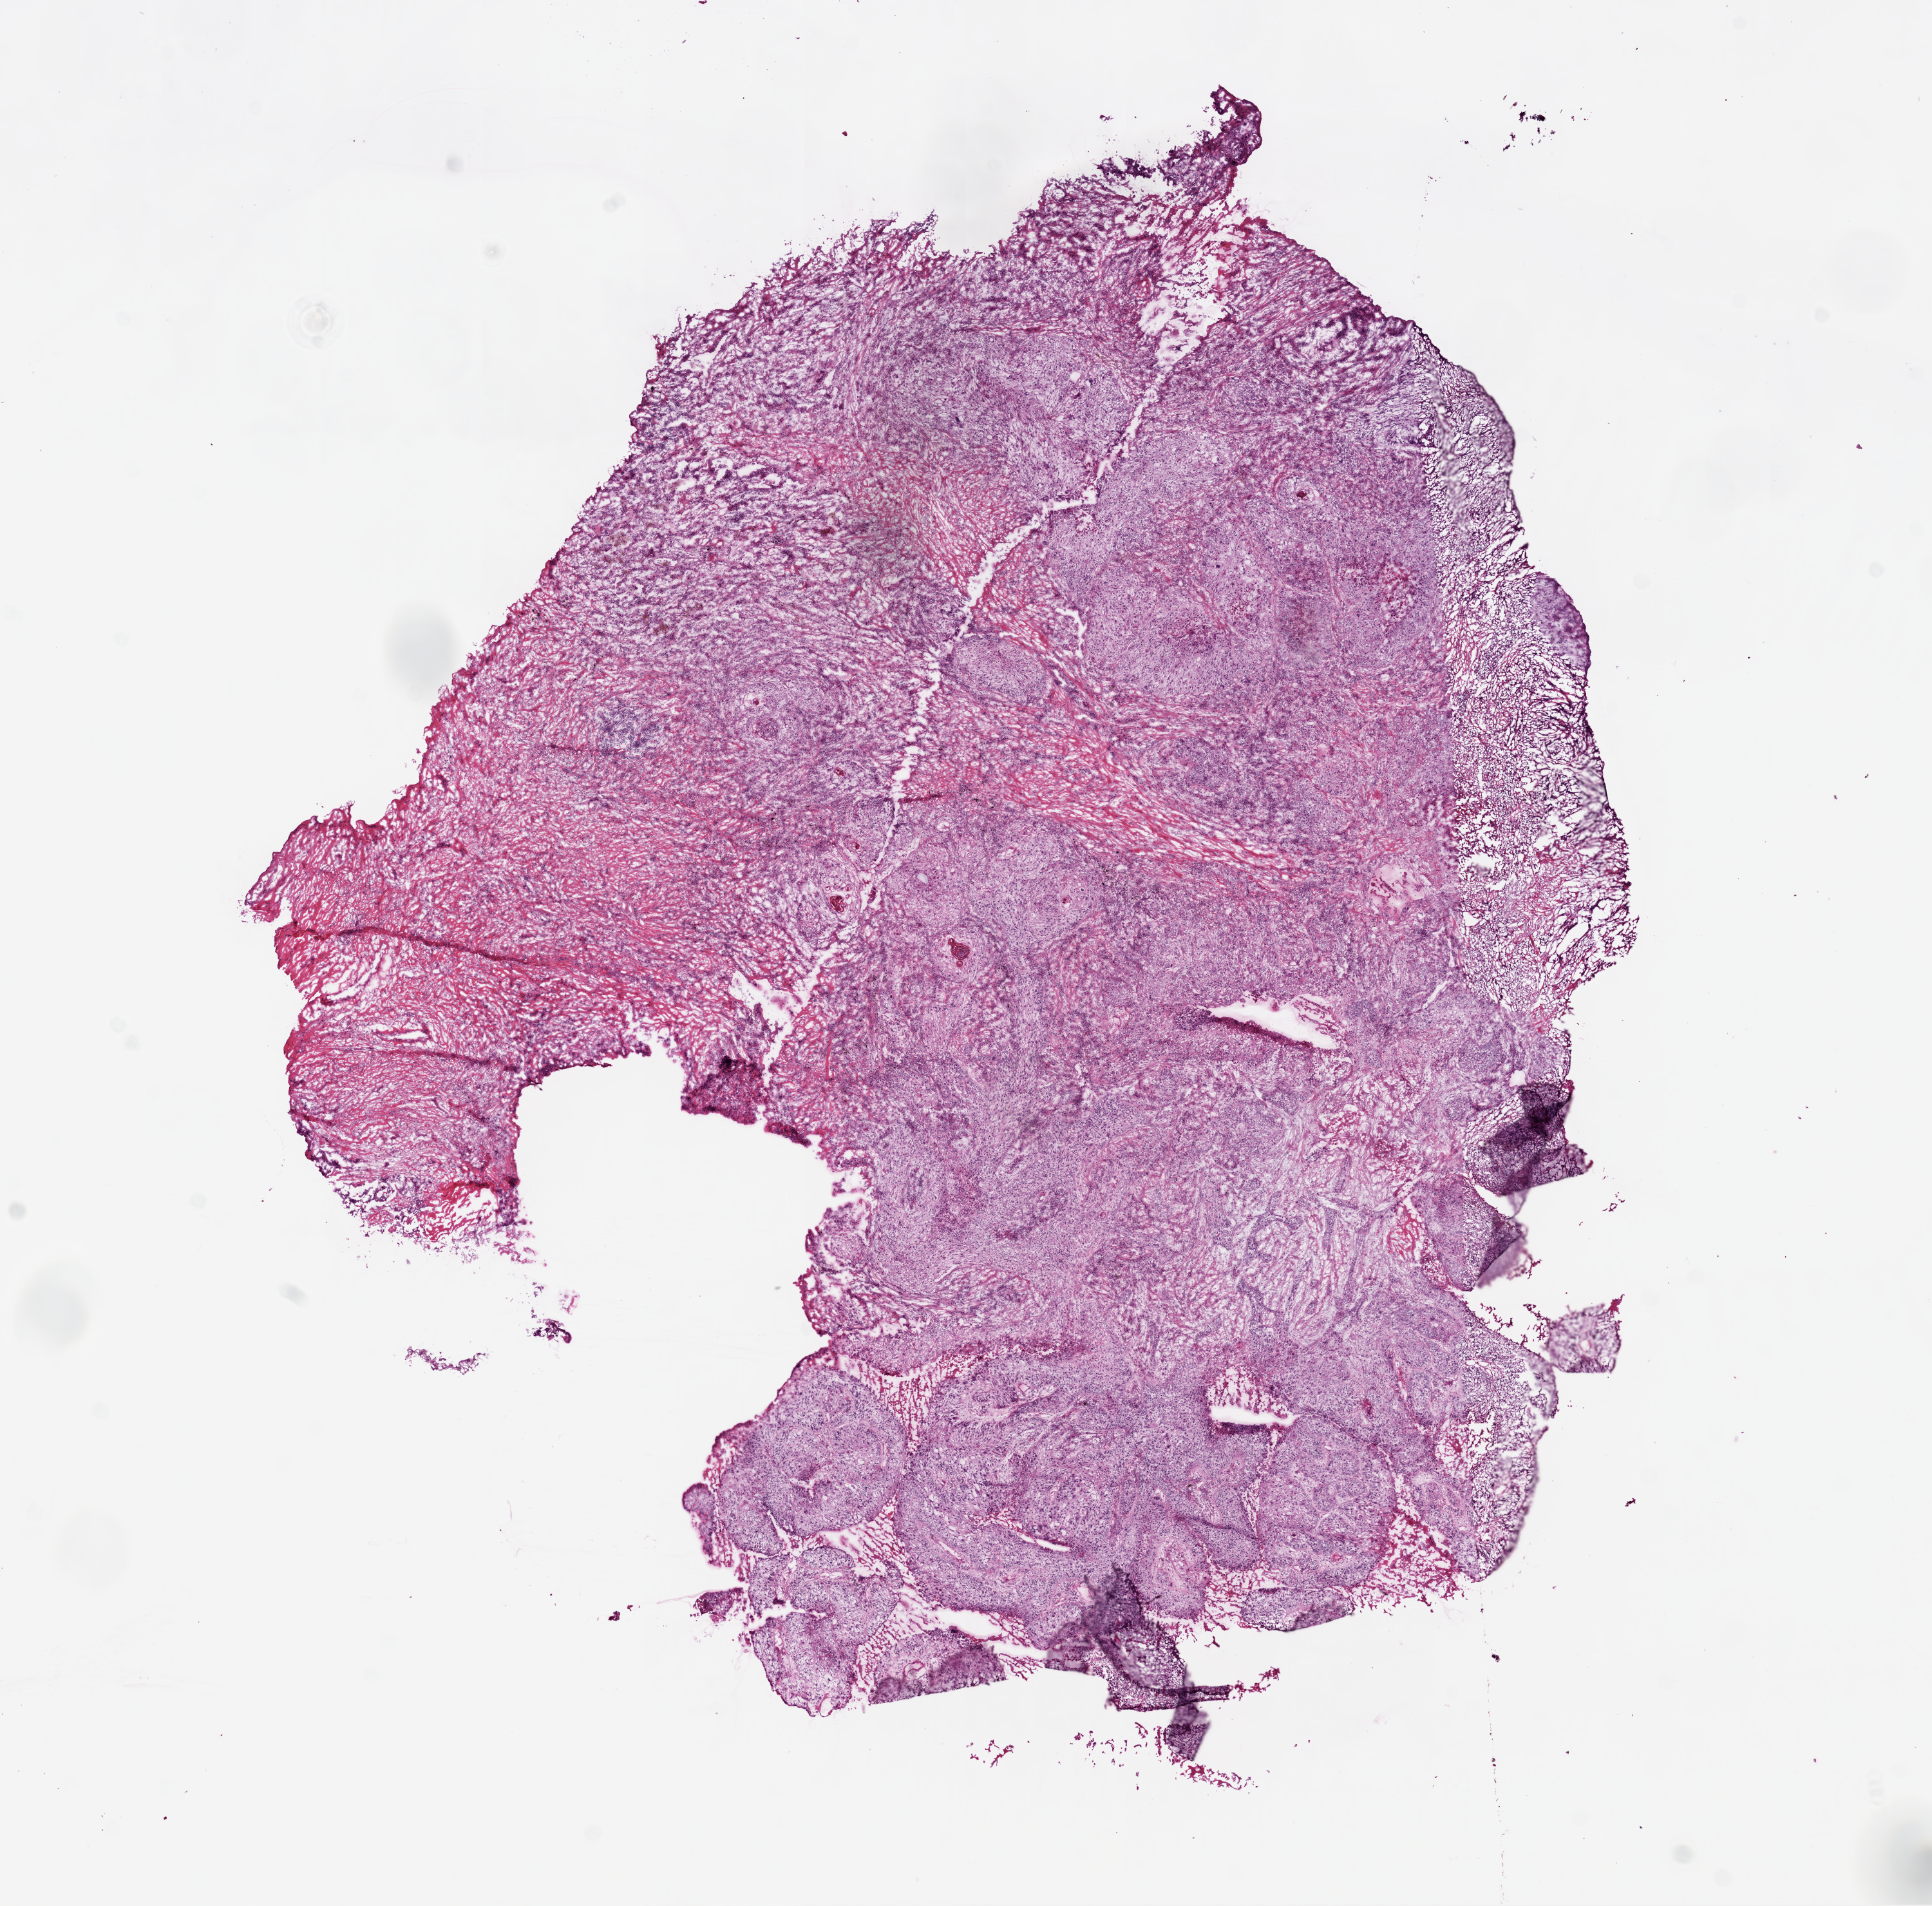
Digitized H&E tissue section (whole slide) — shown as a low-resolution overview of the whole scanned area (about 12.0 x 11.9 mm, acquisition: 20x scan); frozen section; primary tumour sample from the lung. Male, age 64 years at initial diagnosis.
Pathologic diagnosis: Squamous cell carcinoma, NOS (upper lobe, lung).